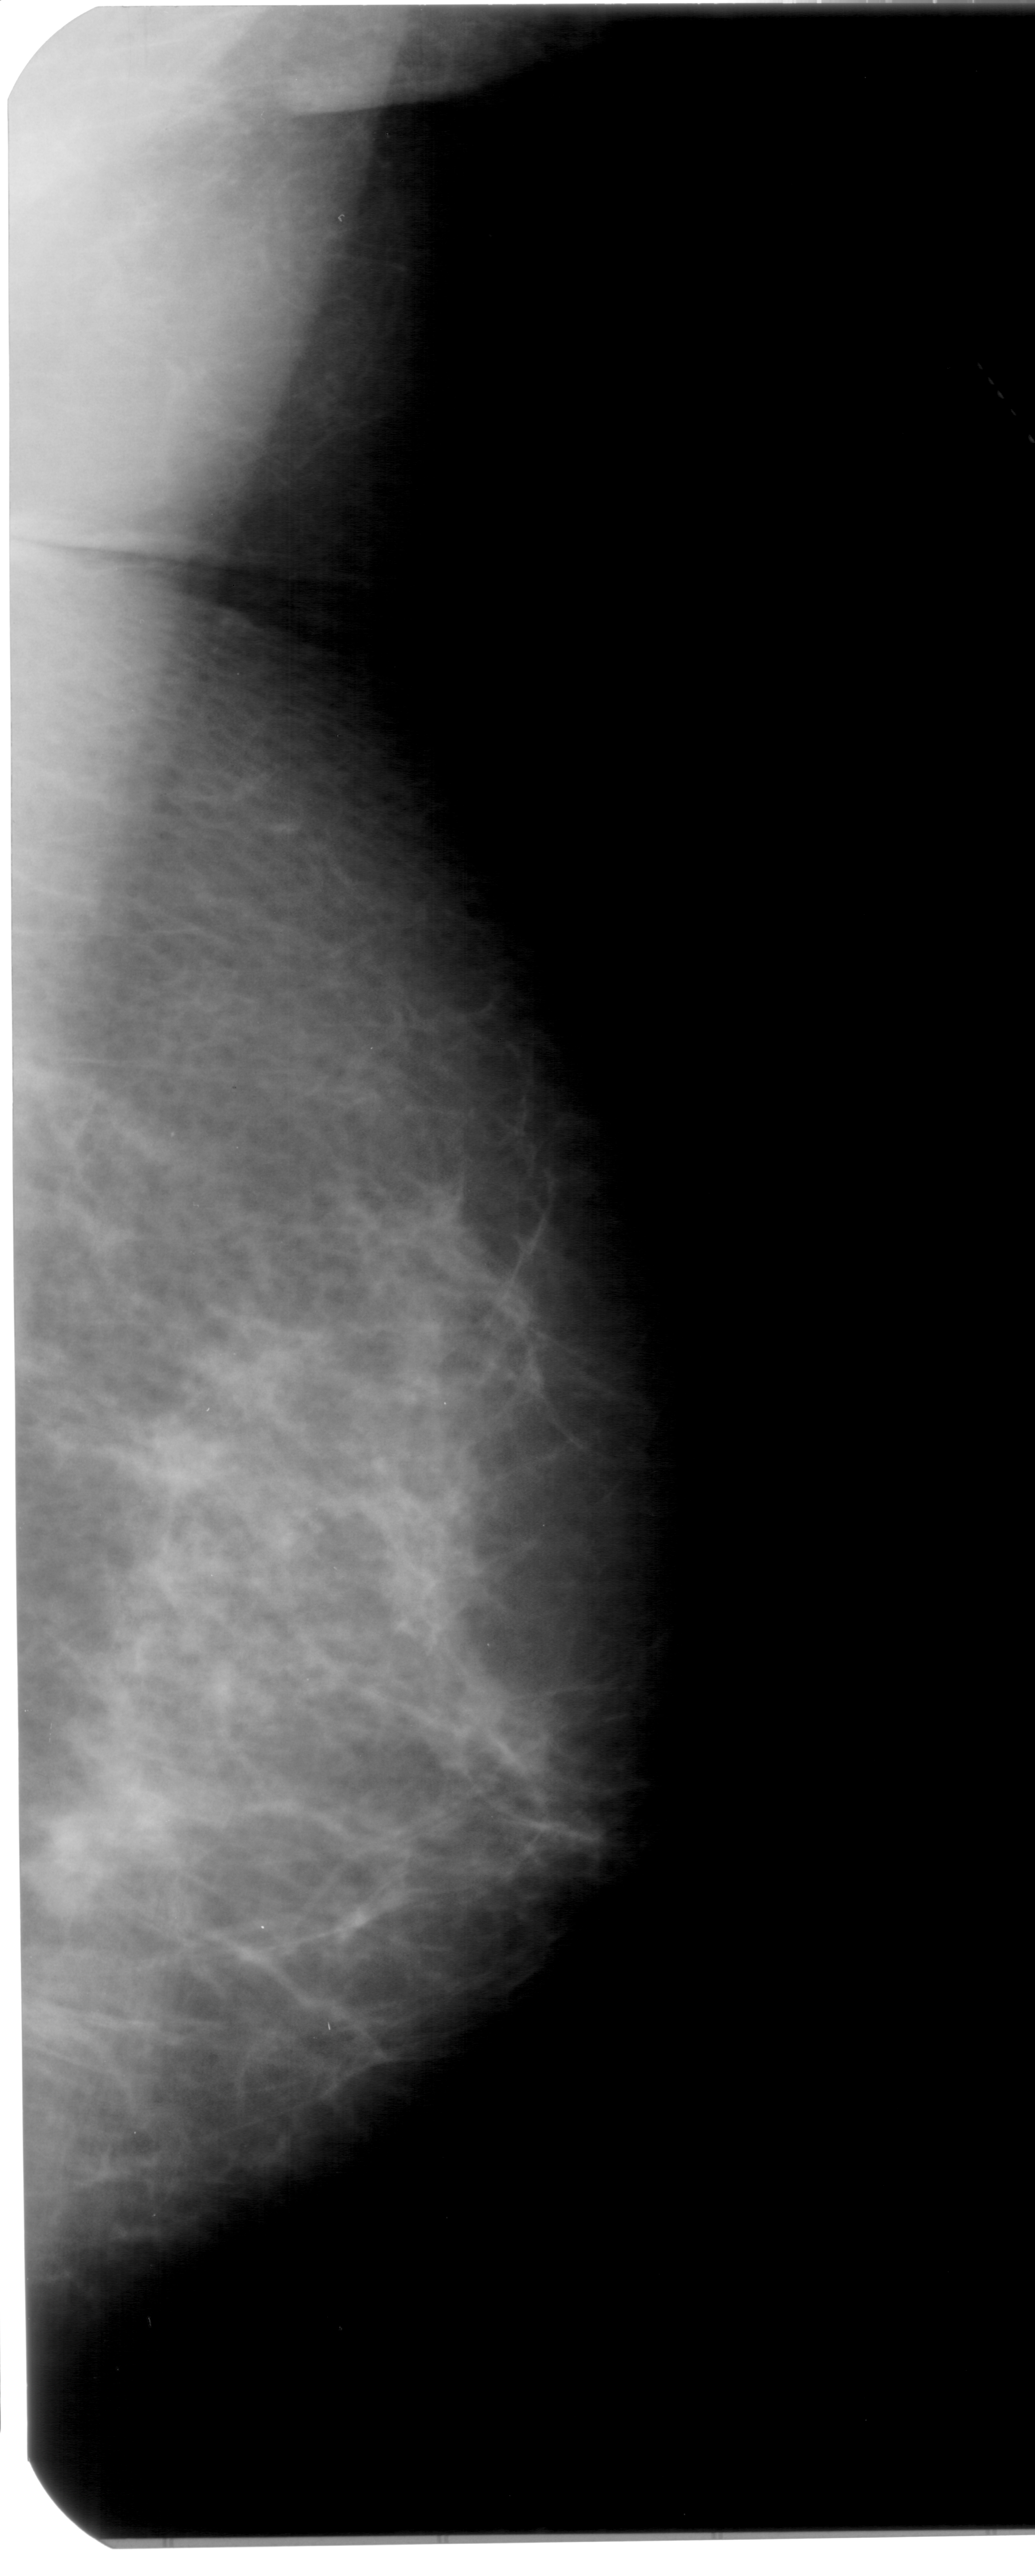
Mammogram (digitized film); right breast; MLO view; breast composition: scattered fibroglandular densities (BI-RADS density category 2 of 4); 1035 × 2576 image matrix.
Marked abnormalities (boxes around the expert regions of interest):
- mass, shape focal asymmetric density, margins ill defined; BI-RADS assessment category 4; pathology (as recorded): benign: bounding box (x1, y1, x2, y2) in pixels: (12, 1776, 121, 1919)